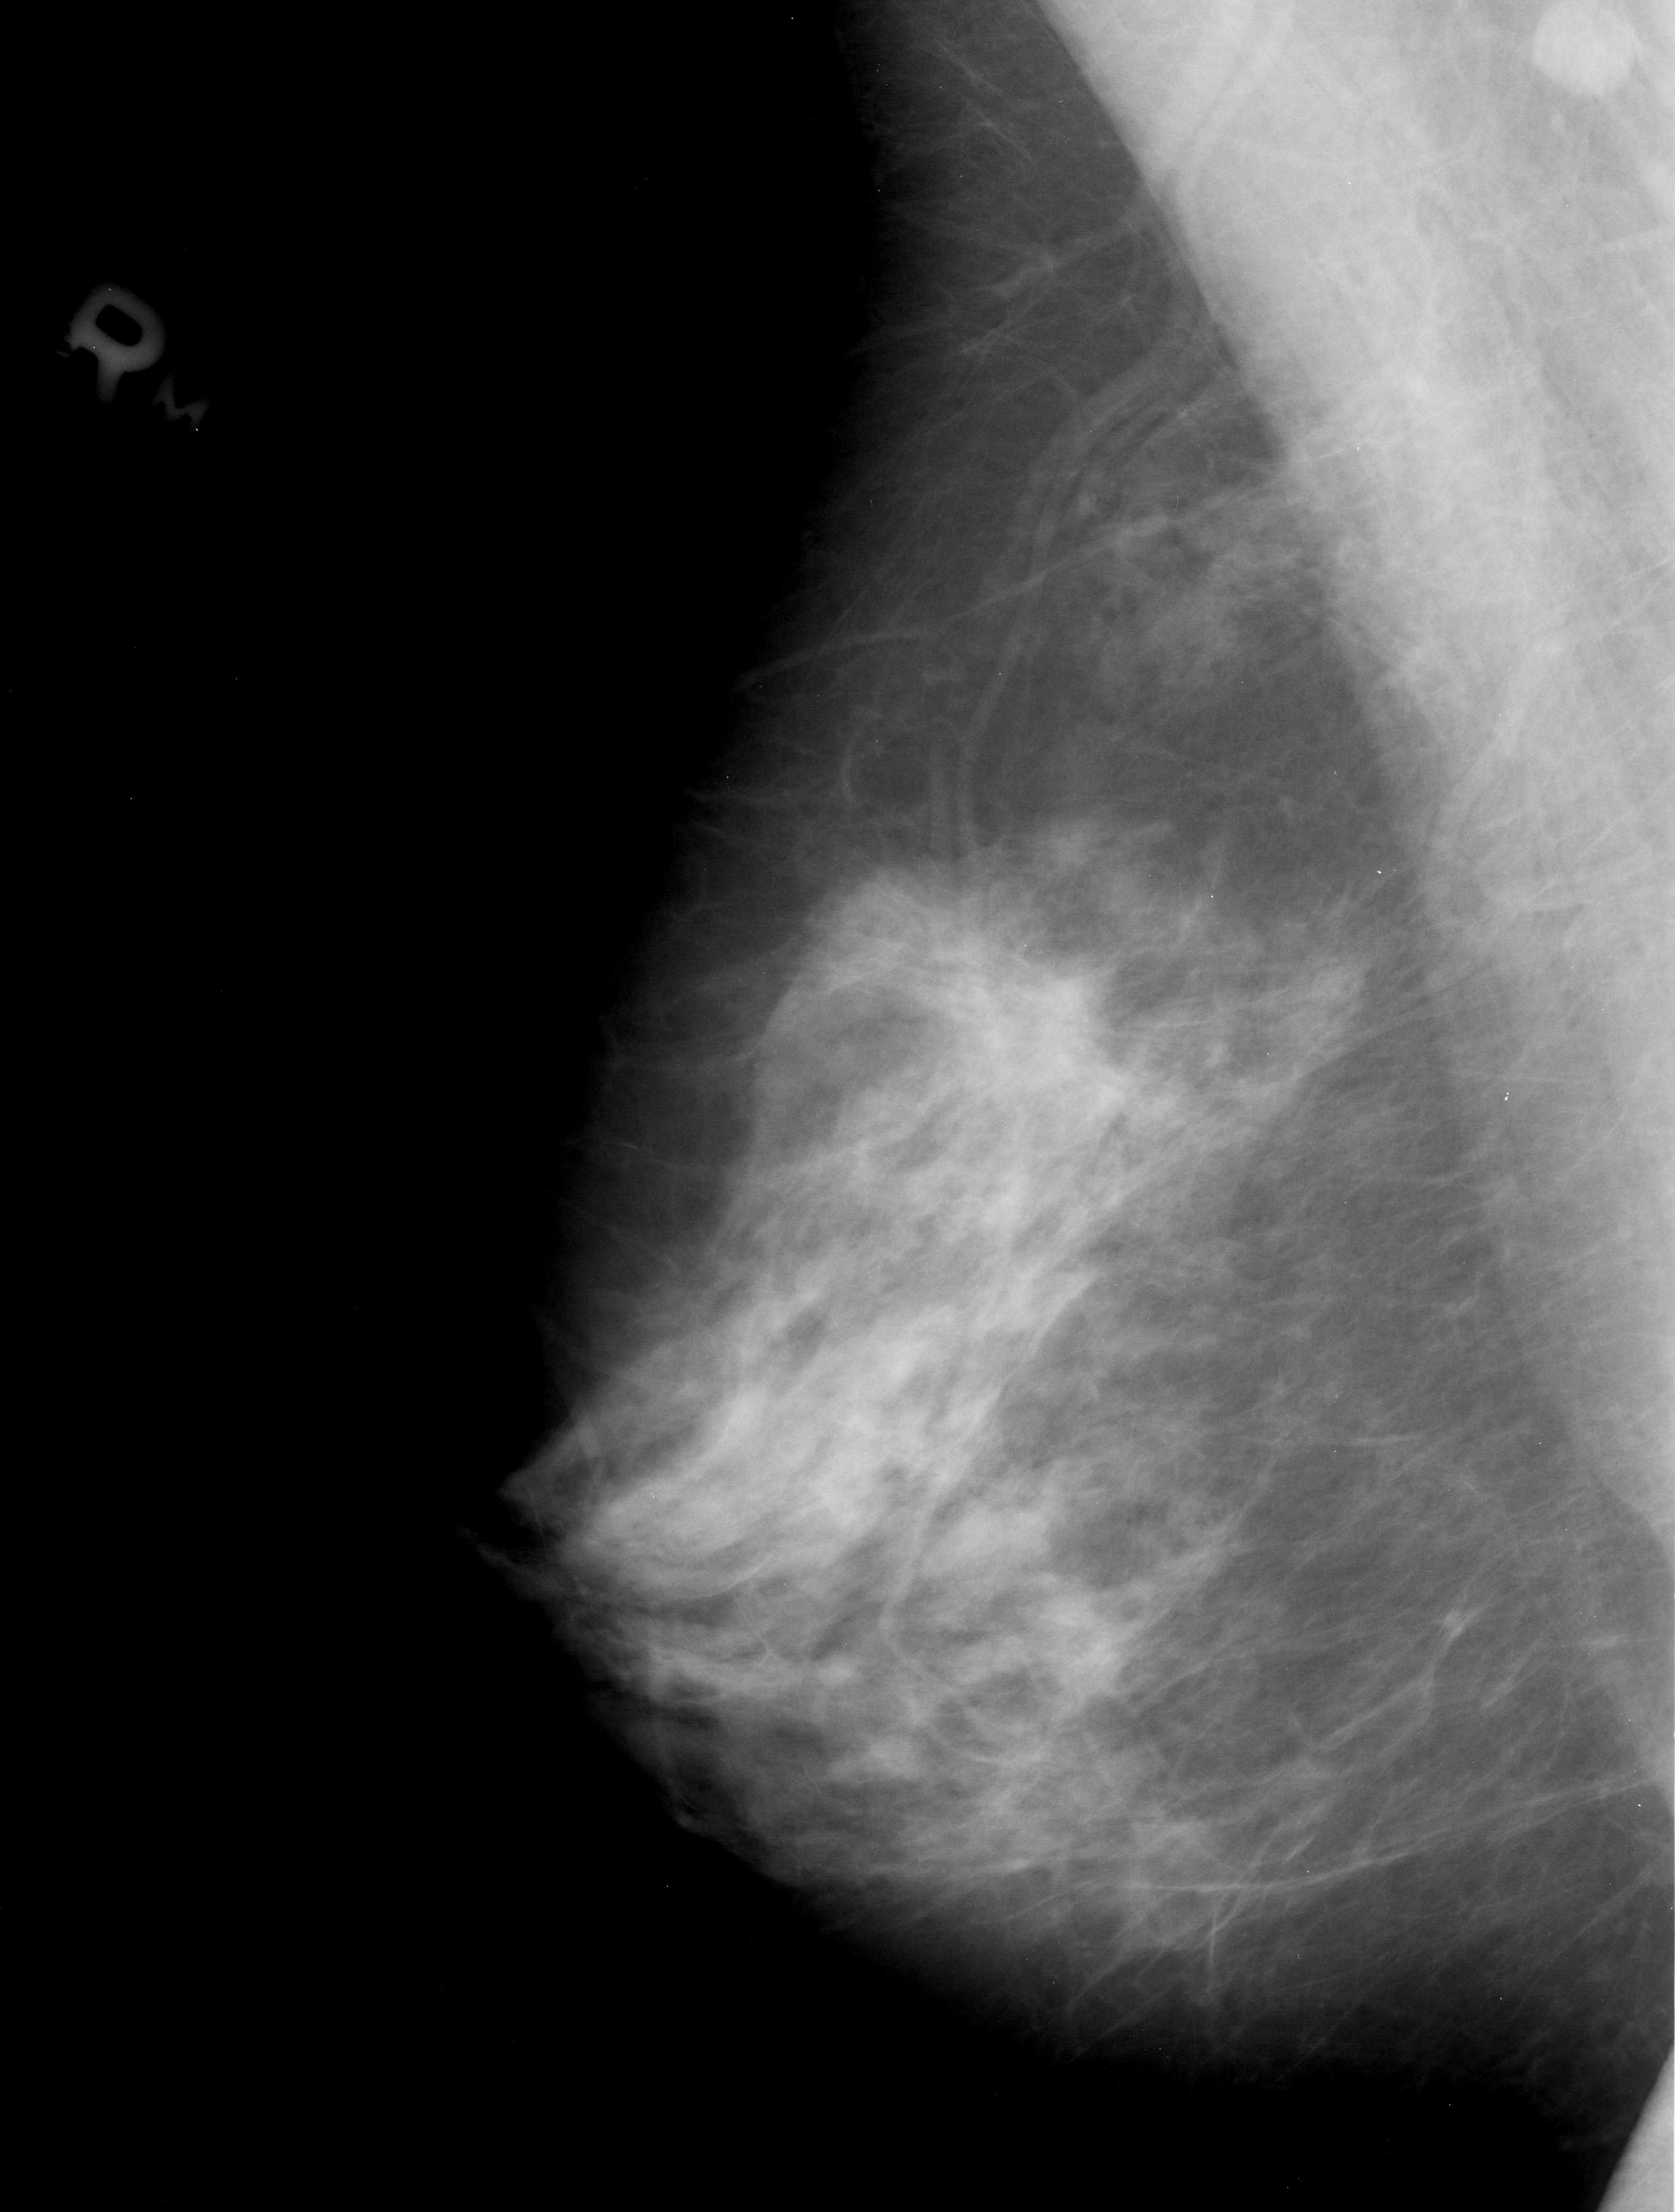
Scanned film-screen mammogram; right breast; mediolateral oblique (MLO) view; breast composition: heterogeneously dense (BI-RADS density category 3 of 4); 1675 × 2212 image matrix.
Expert-marked regions of interest on this image (one box per marked abnormality):
- mass, shape irregular, margins spiculated; BI-RADS assessment category 4; pathology result (as recorded, not read from the image): malignant: bounding box (x1, y1, x2, y2) in pixels: (912, 944, 1096, 1104)